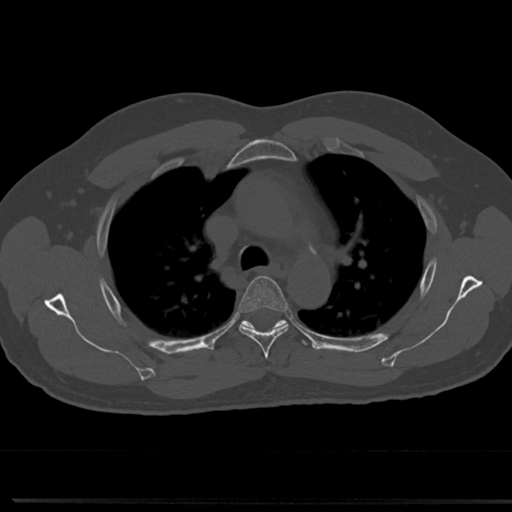
CT including the spine, one axial slice; slice 533 of 817 in the series (ordered by position); bone window (W 1800 / L 400 HU); 0.5 mm slice thickness; 512 × 512 image matrix, field of view 355 × 355 mm. Patient: male, 61 years. From the clinical record (not read from this slice): primary cancer: prostate.
Structures marked on this image (semi-automatically segmented with operator editing):
- T4 vertebra: box from (x=238, y=275) to (x=290, y=355) px
- T5 vertebra: (x=244, y=321)–(x=284, y=327)